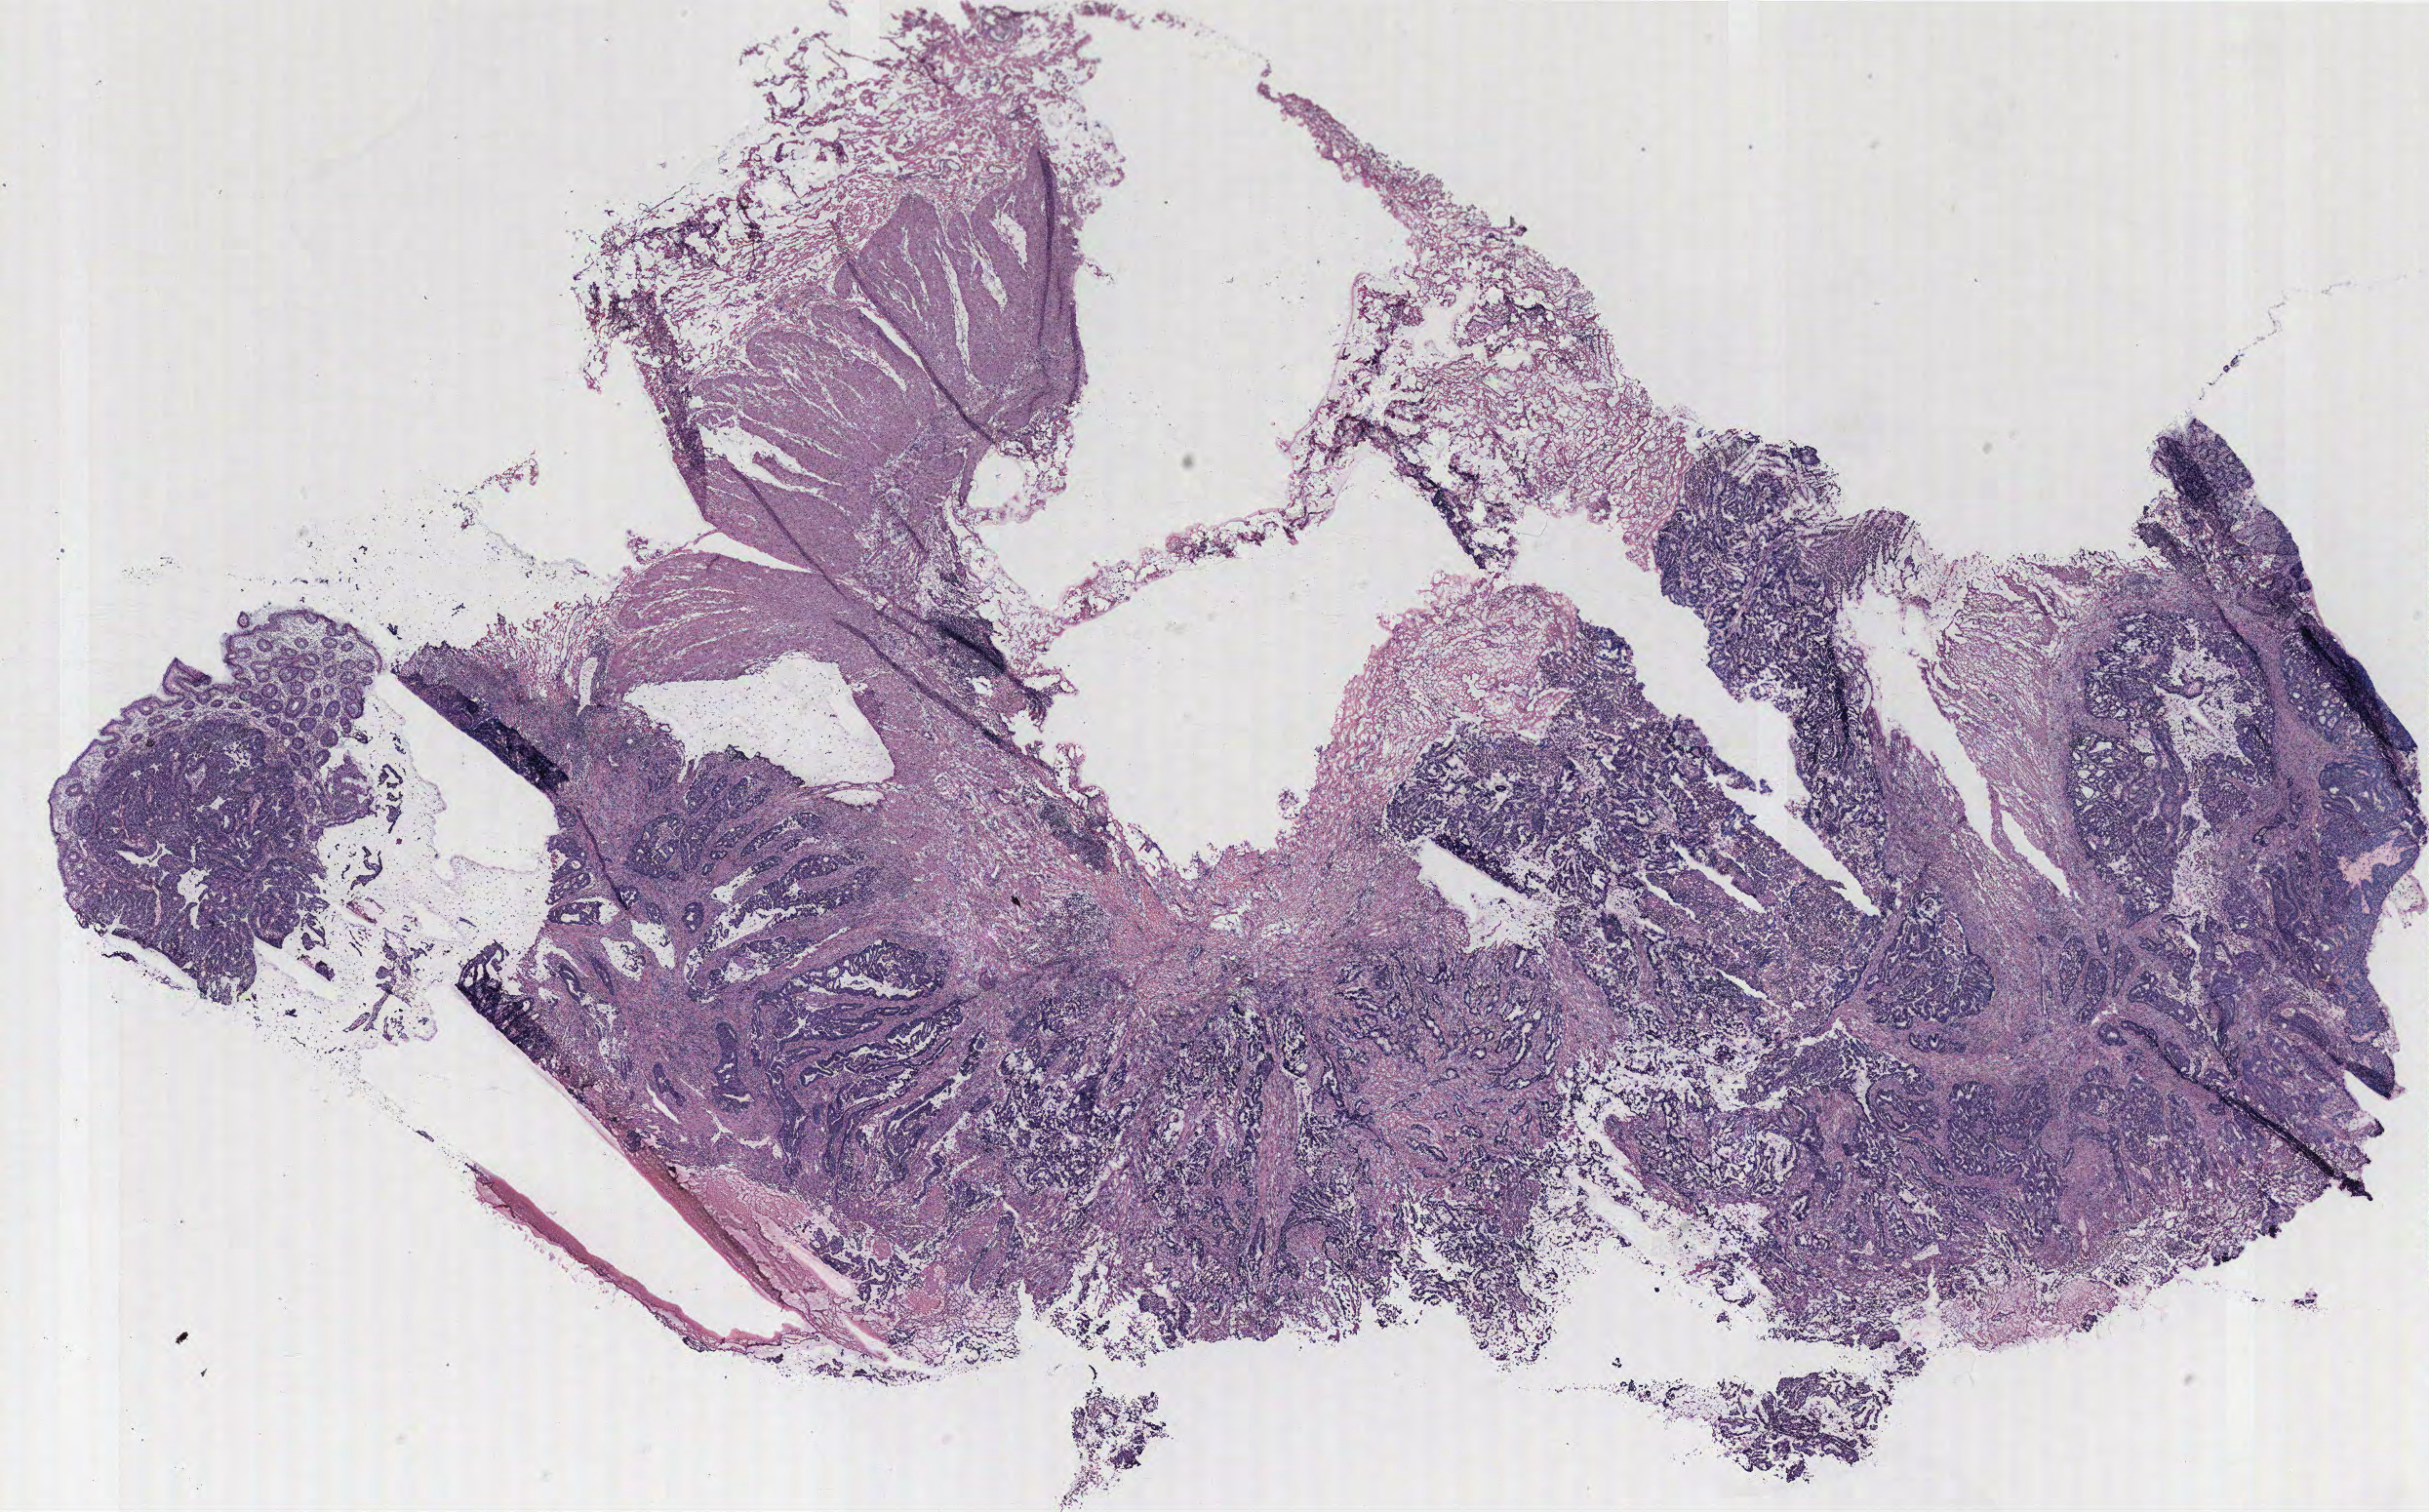
Whole-slide histology image, H&E — whole scanned area (about 19.9 x 12.4 mm, from a 40x scan) shown as a low-resolution overview. Normal (non-tumour) tissue sample, colon. Male, 70 y/o.
This section: normal (non-tumour) tissue from the same patient. Patient diagnosis: Adenocarcinoma, NOS.